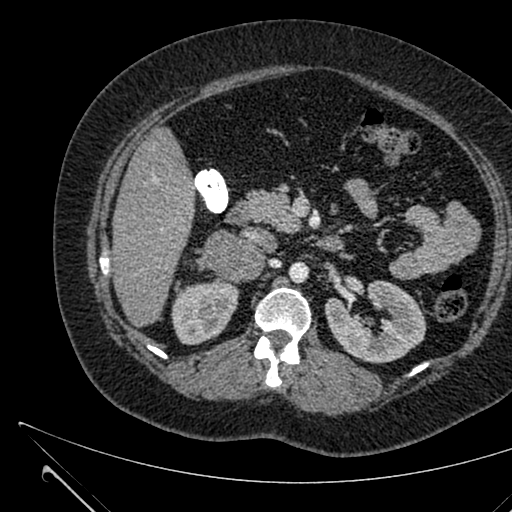
Contrast-enhanced abdominal CT, one axial slice. 120 kVp. Intravenous contrast given. Soft-tissue window (W 400 / L 40 HU). 512 × 512 image matrix. Female patient, age 36 years. Case-level facts recorded for this patient, not image findings: diagnosis: adrenocortical carcinoma; tumour side: right adrenal; tumour size at pathology: 10 cm; Ki-67 index: 20 %; stage (as recorded): 4.
Annotated regions visible in this slice (semi-automatic segmentation, software-assisted and operator-edited):
- mass: bounding box <204,229,264,282> (left, top, right, bottom; pixels)